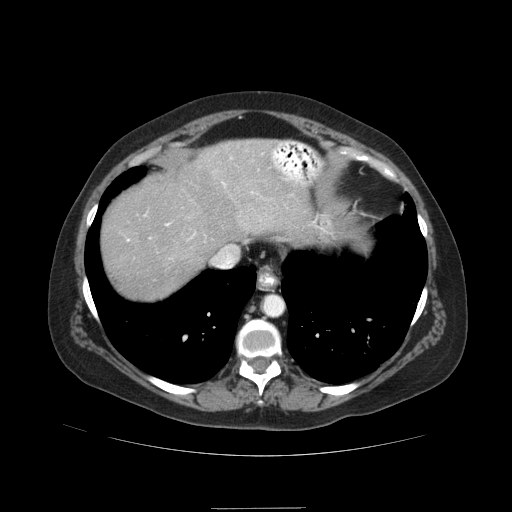
Contrast-enhanced abdominal CT (liver protocol), one axial slice. Reconstruction kernel STANDARD. 120 kVp. Soft-tissue window (W 400 / L 40 HU). 512 × 512 image matrix, field of view 400 × 400 mm. From the clinical record (not read from this slice): diagnosis: hepatocellular carcinoma (patient treated with transarterial chemoembolisation; whether this scan precedes or follows treatment is not stated here); TNM stage (as recorded): Stage-IIIB; Child-Pugh class: A.
Annotated regions visible in this slice (semi-automatic segmentation, software-assisted and operator-edited):
- liver parenchyma outside the tumour (the mass and vessels are separate outlines, so this box may not span the whole liver): bounding box (x1, y1, x2, y2) in pixels: (102, 138, 312, 298)
- liver vessels: (127, 182, 225, 241)